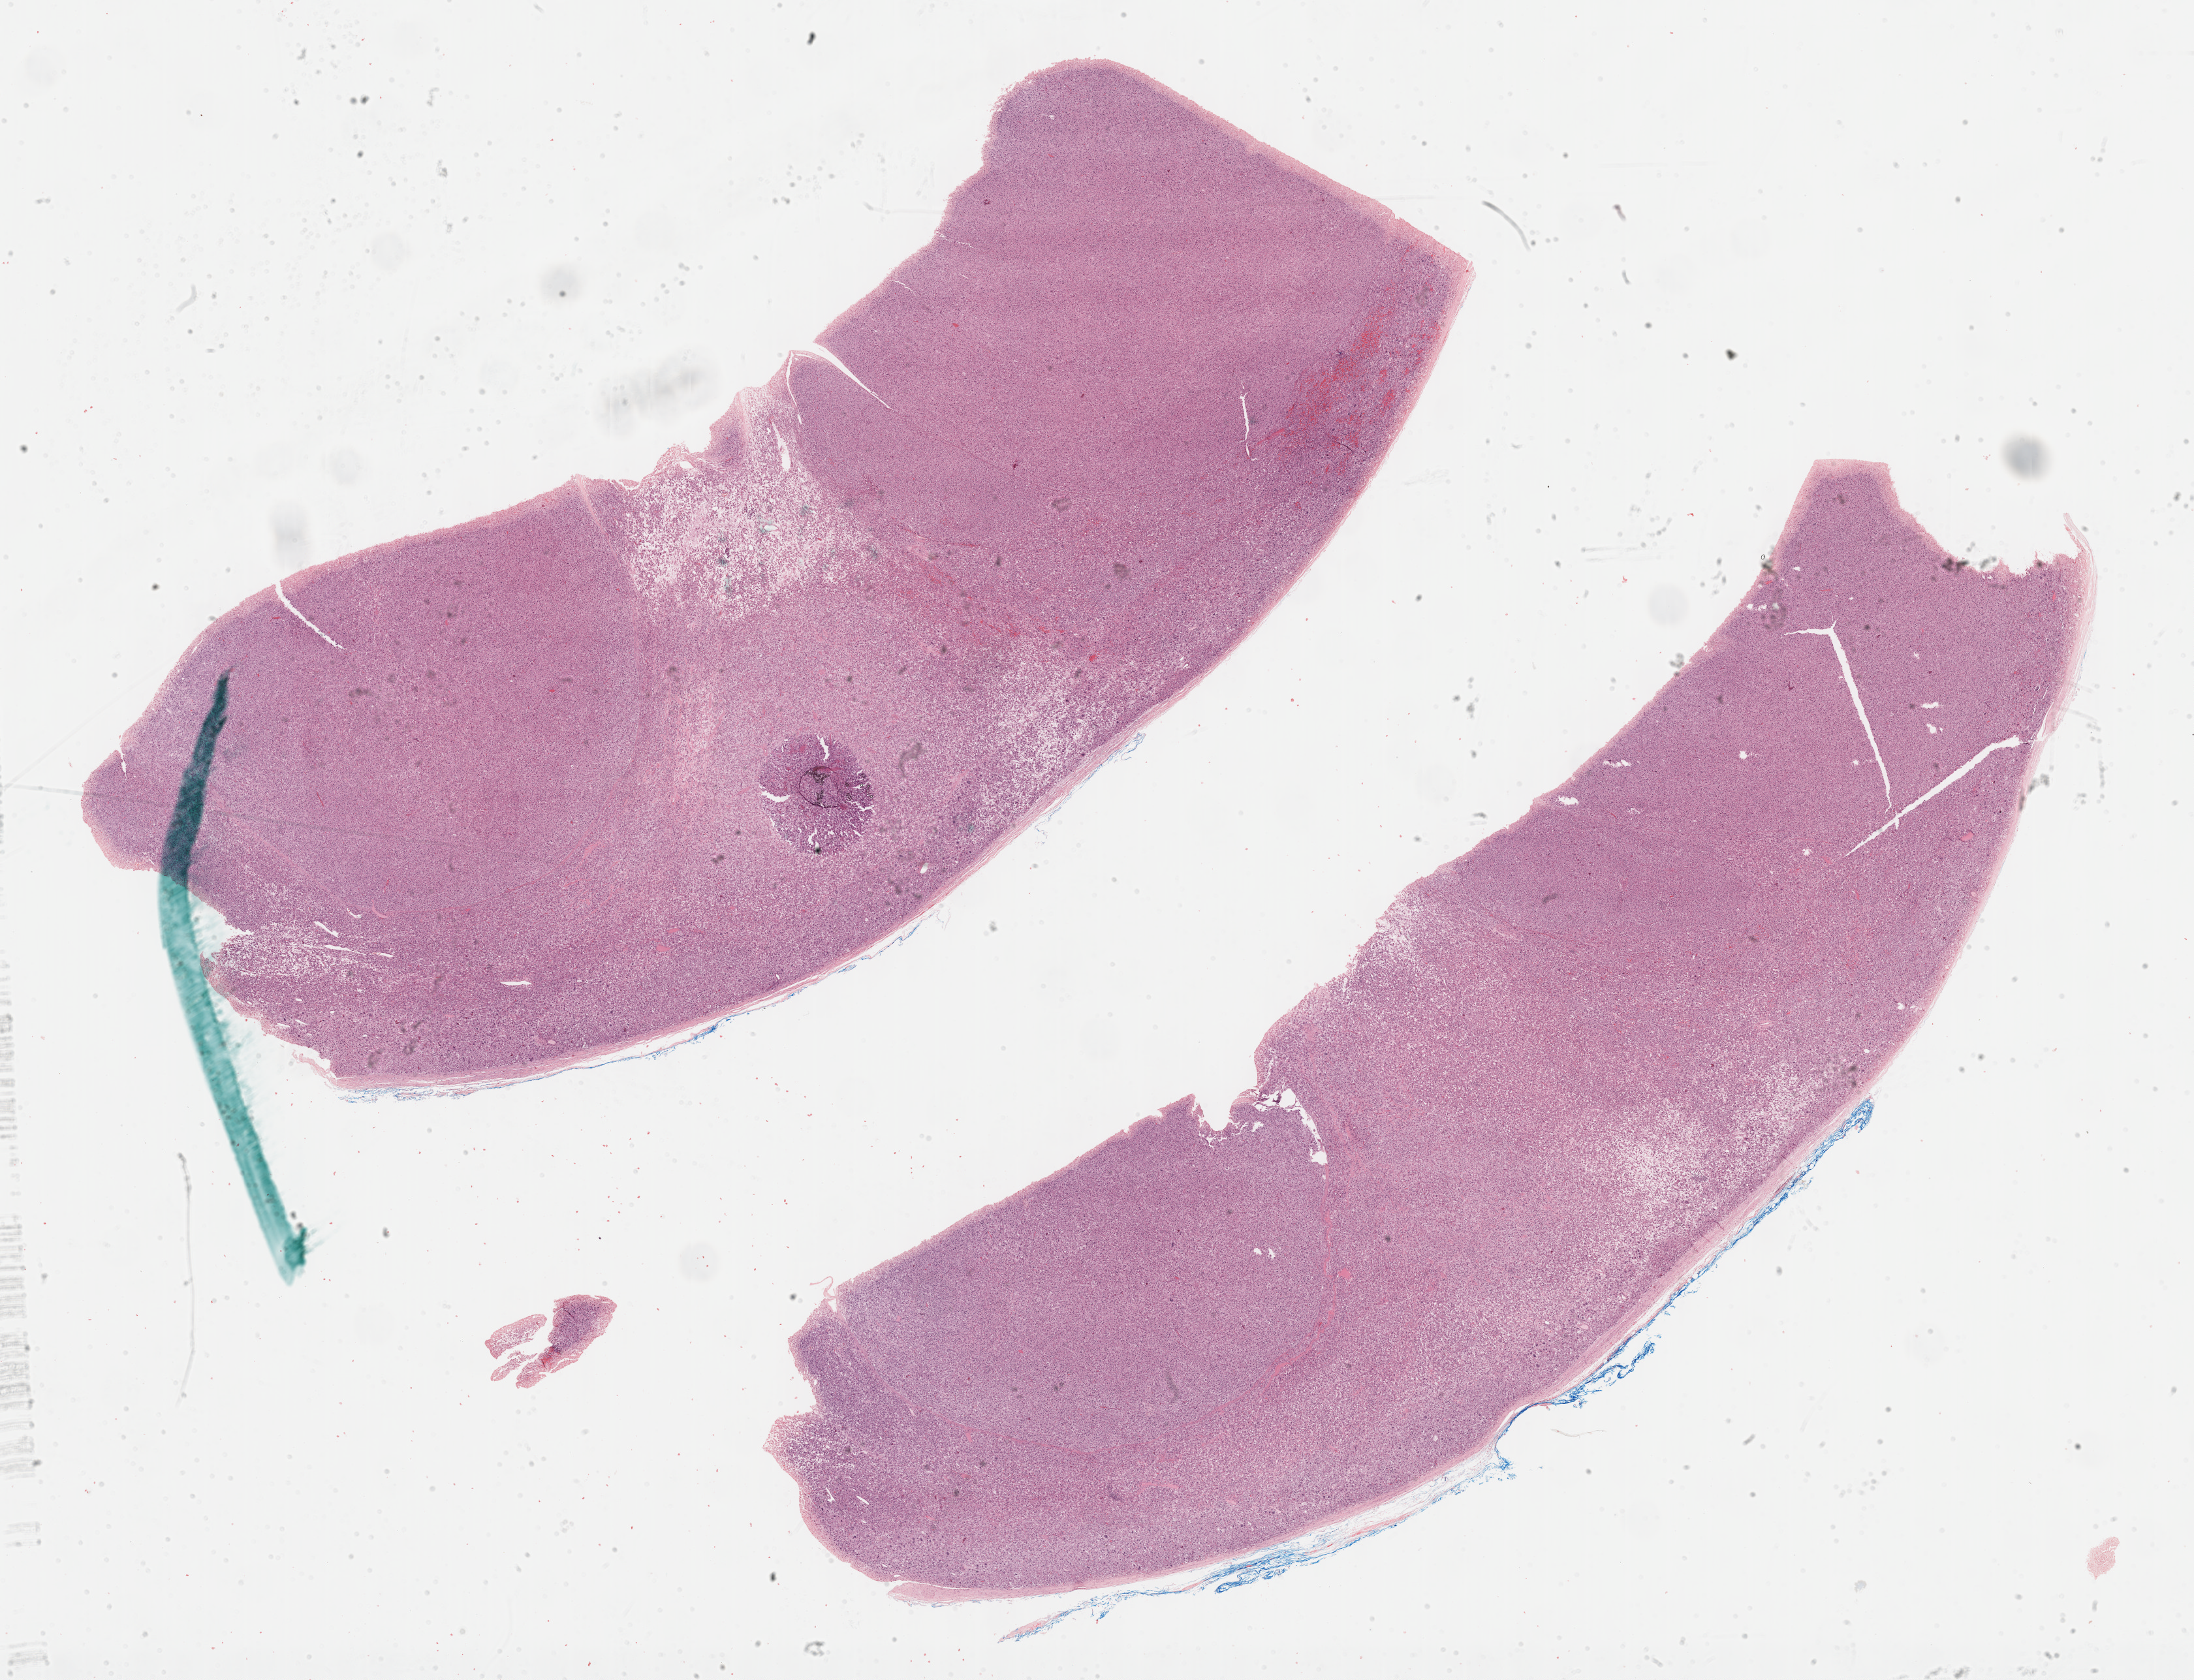
Digitized Hematoxylin and eosin (H&E) stained tissue section (whole slide) — a low-resolution overview of the entire scanned area, about 27.2 x 20.8 mm. Formalin-fixed paraffin-embedded (FFPE) diagnostic section. Sample: primary tumour, adrenal cortex. Male patient; age at initial diagnosis 45 years.
Histologic diagnosis: Adrenal cortical carcinoma.